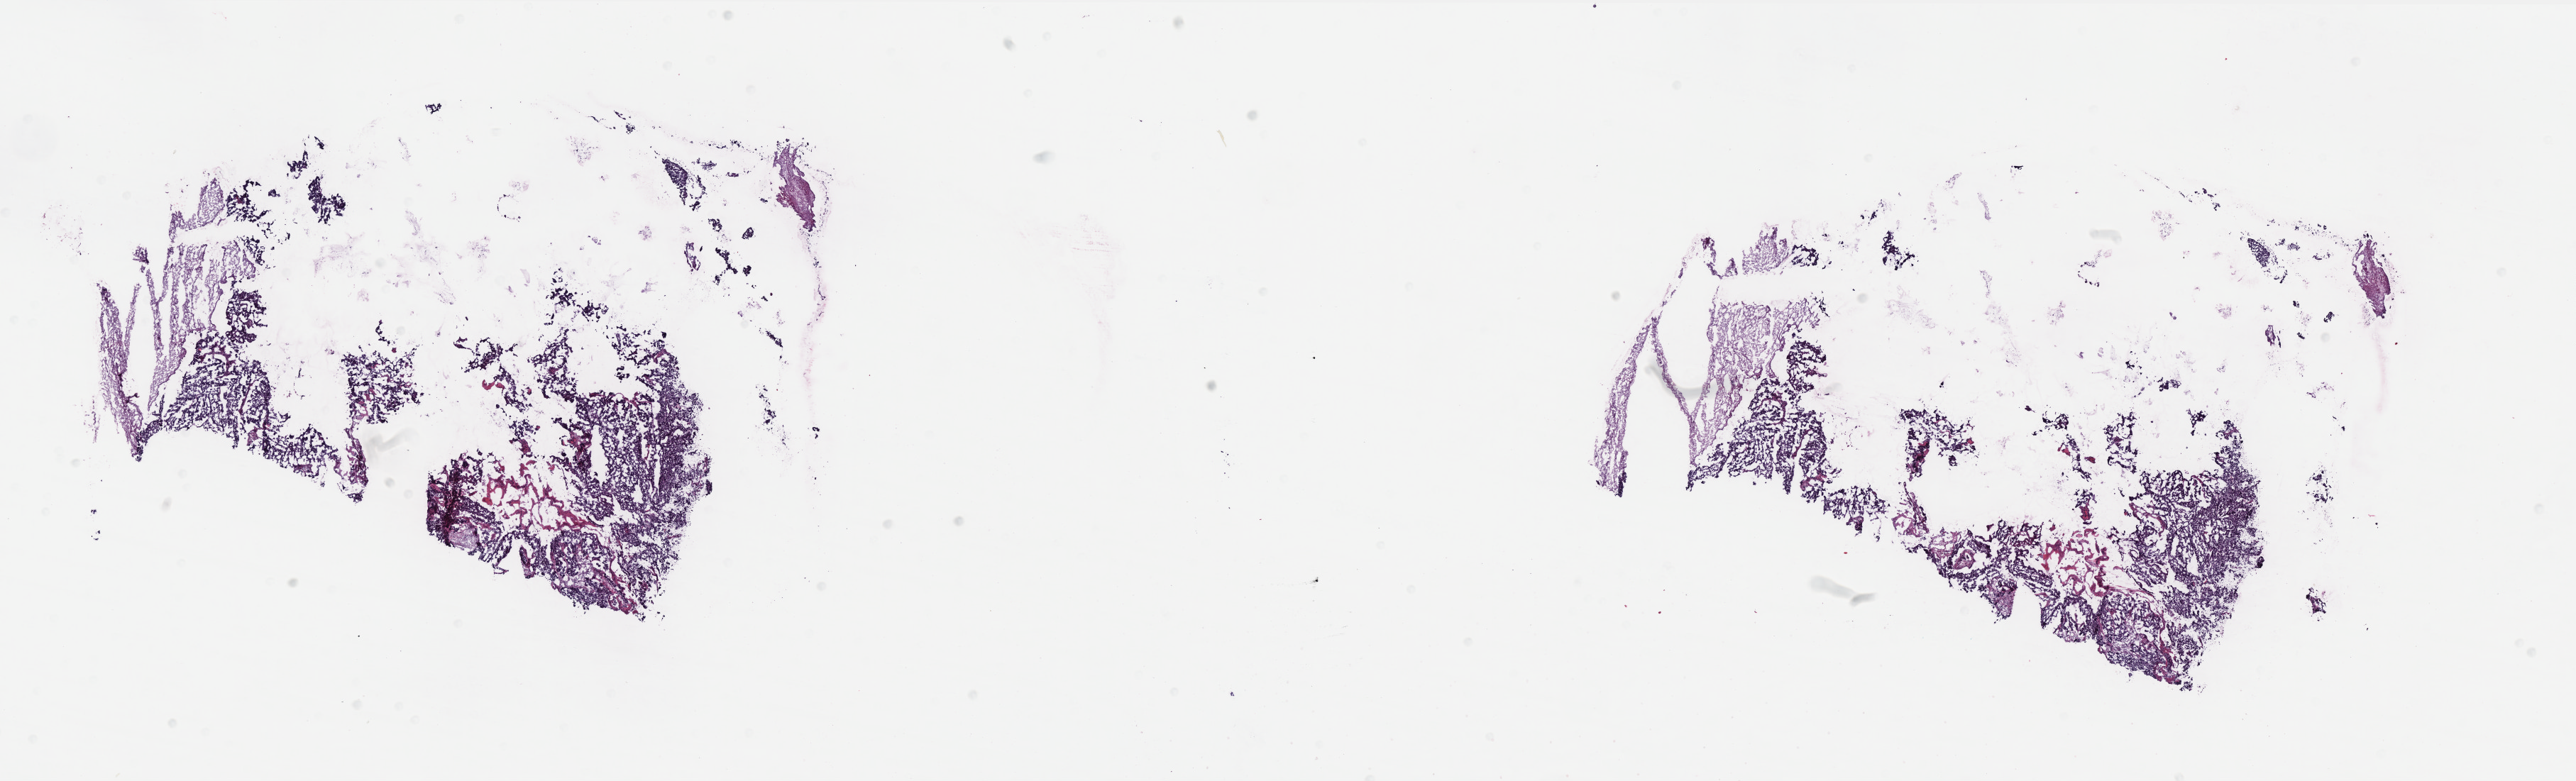
Digitized H&E-stained tissue section (whole slide) — shown as a low-resolution overview of the whole scanned area (about 29.1 x 8.8 mm), frozen section from the bottom of the tissue portion, uterus, primary tumour sample. Patient: female, age at initial diagnosis 54 years. Histologic grade: G3 (poorly differentiated). Slide review estimates, as recorded: tumour cells 80%, tumour nuclei 90%, normal cells 0%, stromal cells 0%, necrosis 20%. Infiltration values recorded for this section: lymphocyte infiltration 0%, monocyte infiltration 0%, neutrophil infiltration 0%.
- FIGO stage: IA
- pathologic diagnosis: Endometrioid adenocarcinoma, NOS (endometrium)
- lymph nodes positive (case pathology): 0 of 2 examined